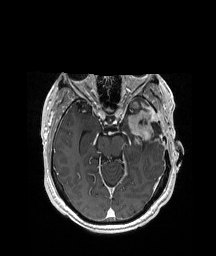
Brain MRI from a brain-tumour surgery series, one axial slice. T1-weighted post-contrast. 1 mm slice thickness. 216 × 256 image matrix, field of view 228 × 270 mm. Case-level facts recorded for this patient, not image findings: histopathology: Glioblastoma; WHO grade: 4; IDH mutation: no; tumour location: Left Anterior/Superior Temporal.
Annotated regions visible in this slice (manually delineated by an expert):
- previous resection cavity: bounding box <139,118,161,135> (left, top, right, bottom; pixels)
- tumour: <123,99,158,144>